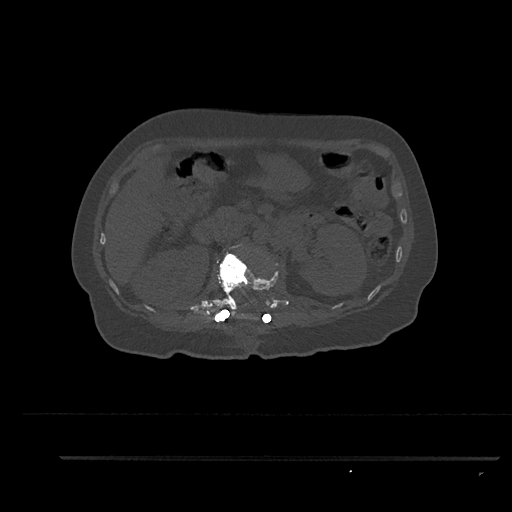
CT including the spine, one axial slice. Slice 203 of 797 in the series (ordered by position). Reconstruction kernel Br40s/3. 120 kVp. Bone window (W 1800 / L 400 HU). 0.5 mm slice thickness. 512 × 512 image matrix, field of view 408 × 408 mm. Female patient, age 44 years. Case-level facts recorded for this patient, not image findings: primary cancer: renal; vertebrae with lytic lesions (as recorded): L1.
Structures marked on this image (semi-automatic segmentation, software-assisted and operator-edited):
- L1 vertebra: box from (x=216, y=243) to (x=279, y=319) px